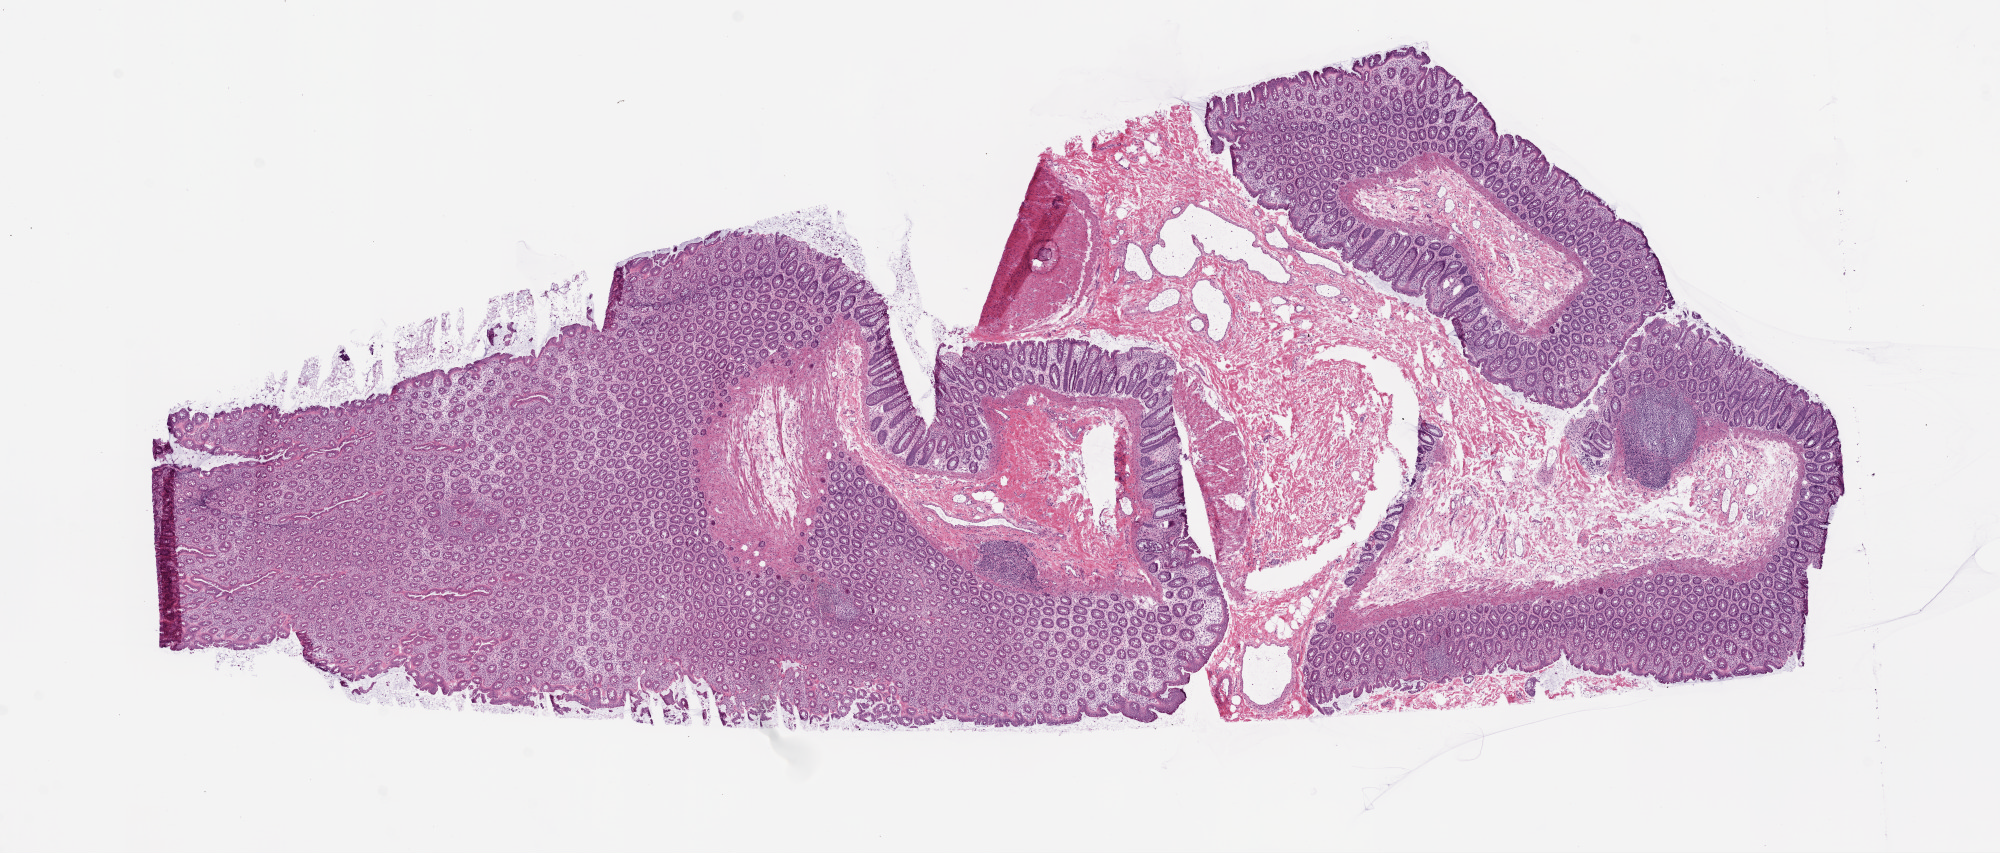
Whole-slide histology image, H&E-stained, low-resolution overview of the scanned area, about 16.0 x 6.8 mm (acquisition: 20x scan); frozen section from the top of the tissue portion; sample: solid tissue normal (non-tumour tissue), colon. Patient: female, age at initial diagnosis 40 years.
This section: solid tissue normal sample (biorepository sample class). Patient diagnosis: Adenocarcinoma, NOS.